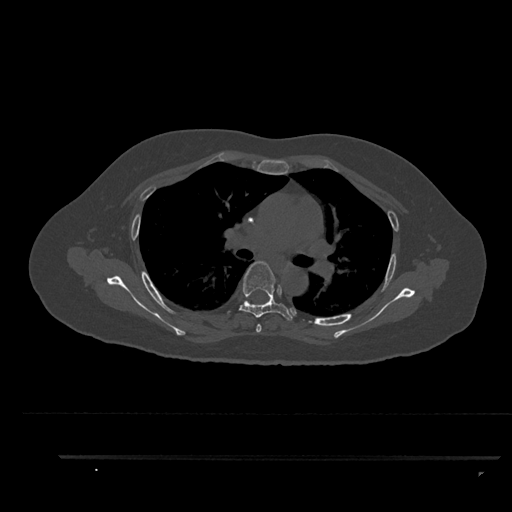
CT including the spine, one axial slice; position 605 of 797 along the scan axis; reconstruction kernel Br40s/3; bone window (W 1800 / L 400 HU); 0.5 mm slice thickness; 512 × 512 image matrix, field of view 408 × 408 mm. Female patient, age 44 years. Case-level facts recorded for this patient, not image findings: primary cancer: renal.
Annotated regions visible in this slice (semi-automatically segmented with operator editing):
- T4 vertebra: bounding box (x1, y1, x2, y2) in pixels: (256, 324, 262, 333)
- T5 vertebra: (227, 261, 293, 321)